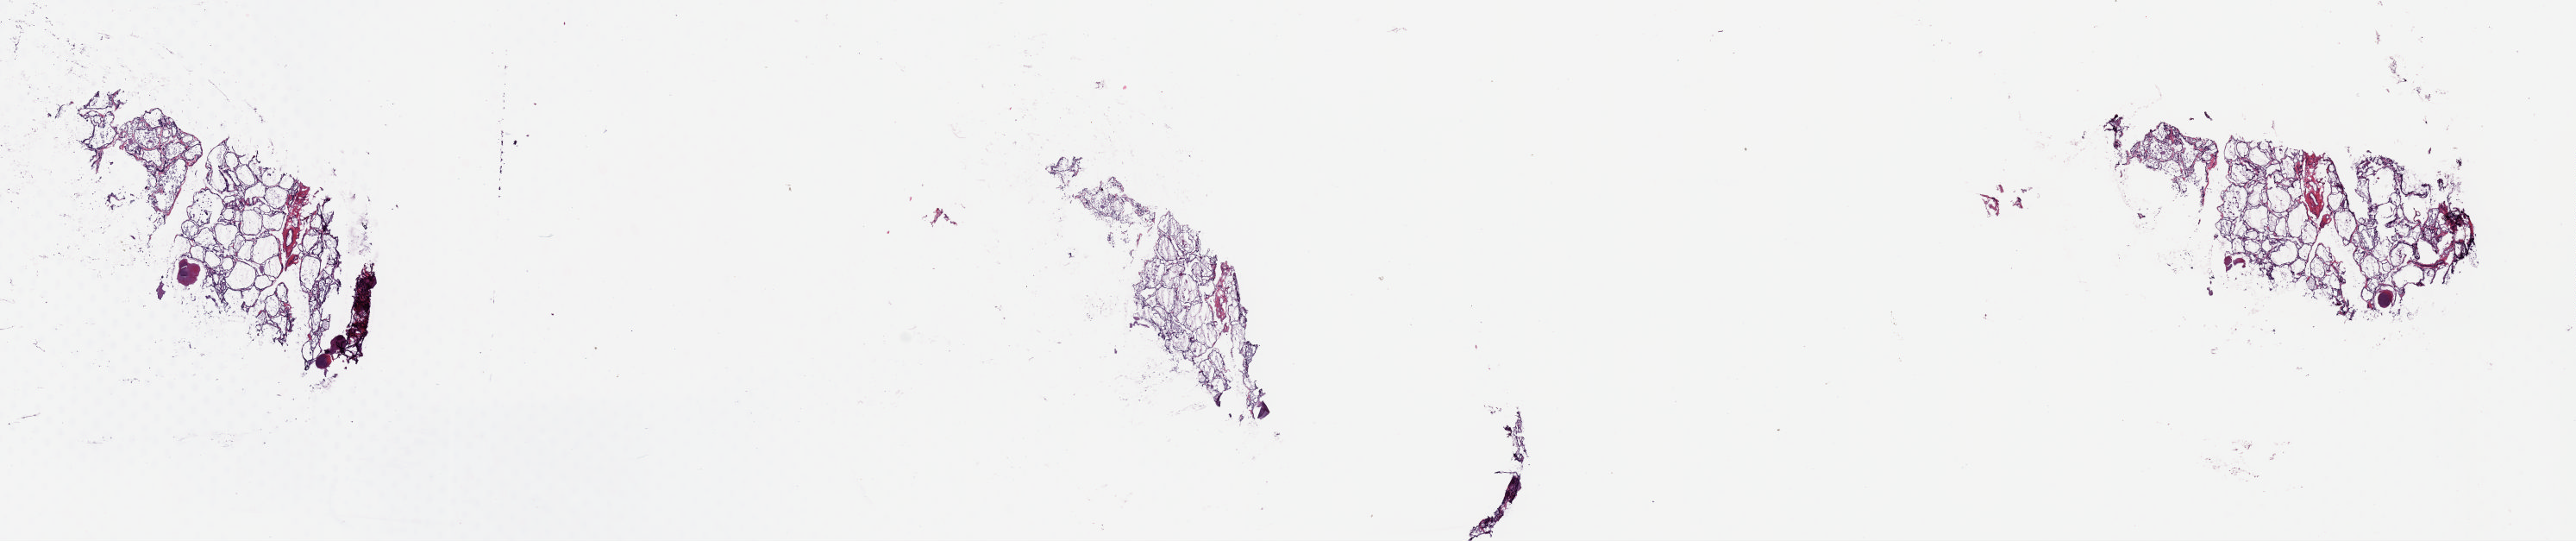
Whole-slide histology image, H&E-stained — low-resolution overview of the scanned area, about 23.6 x 4.9 mm (acquisition: 20x scan), frozen section from the top of the tissue portion, solid tissue normal (non-tumour tissue) sample from the thyroid. Male patient; age at initial diagnosis 41 years.
This section: solid tissue normal sample (biorepository sample class). Patient diagnosis: Papillary adenocarcinoma, NOS (thyroid gland).